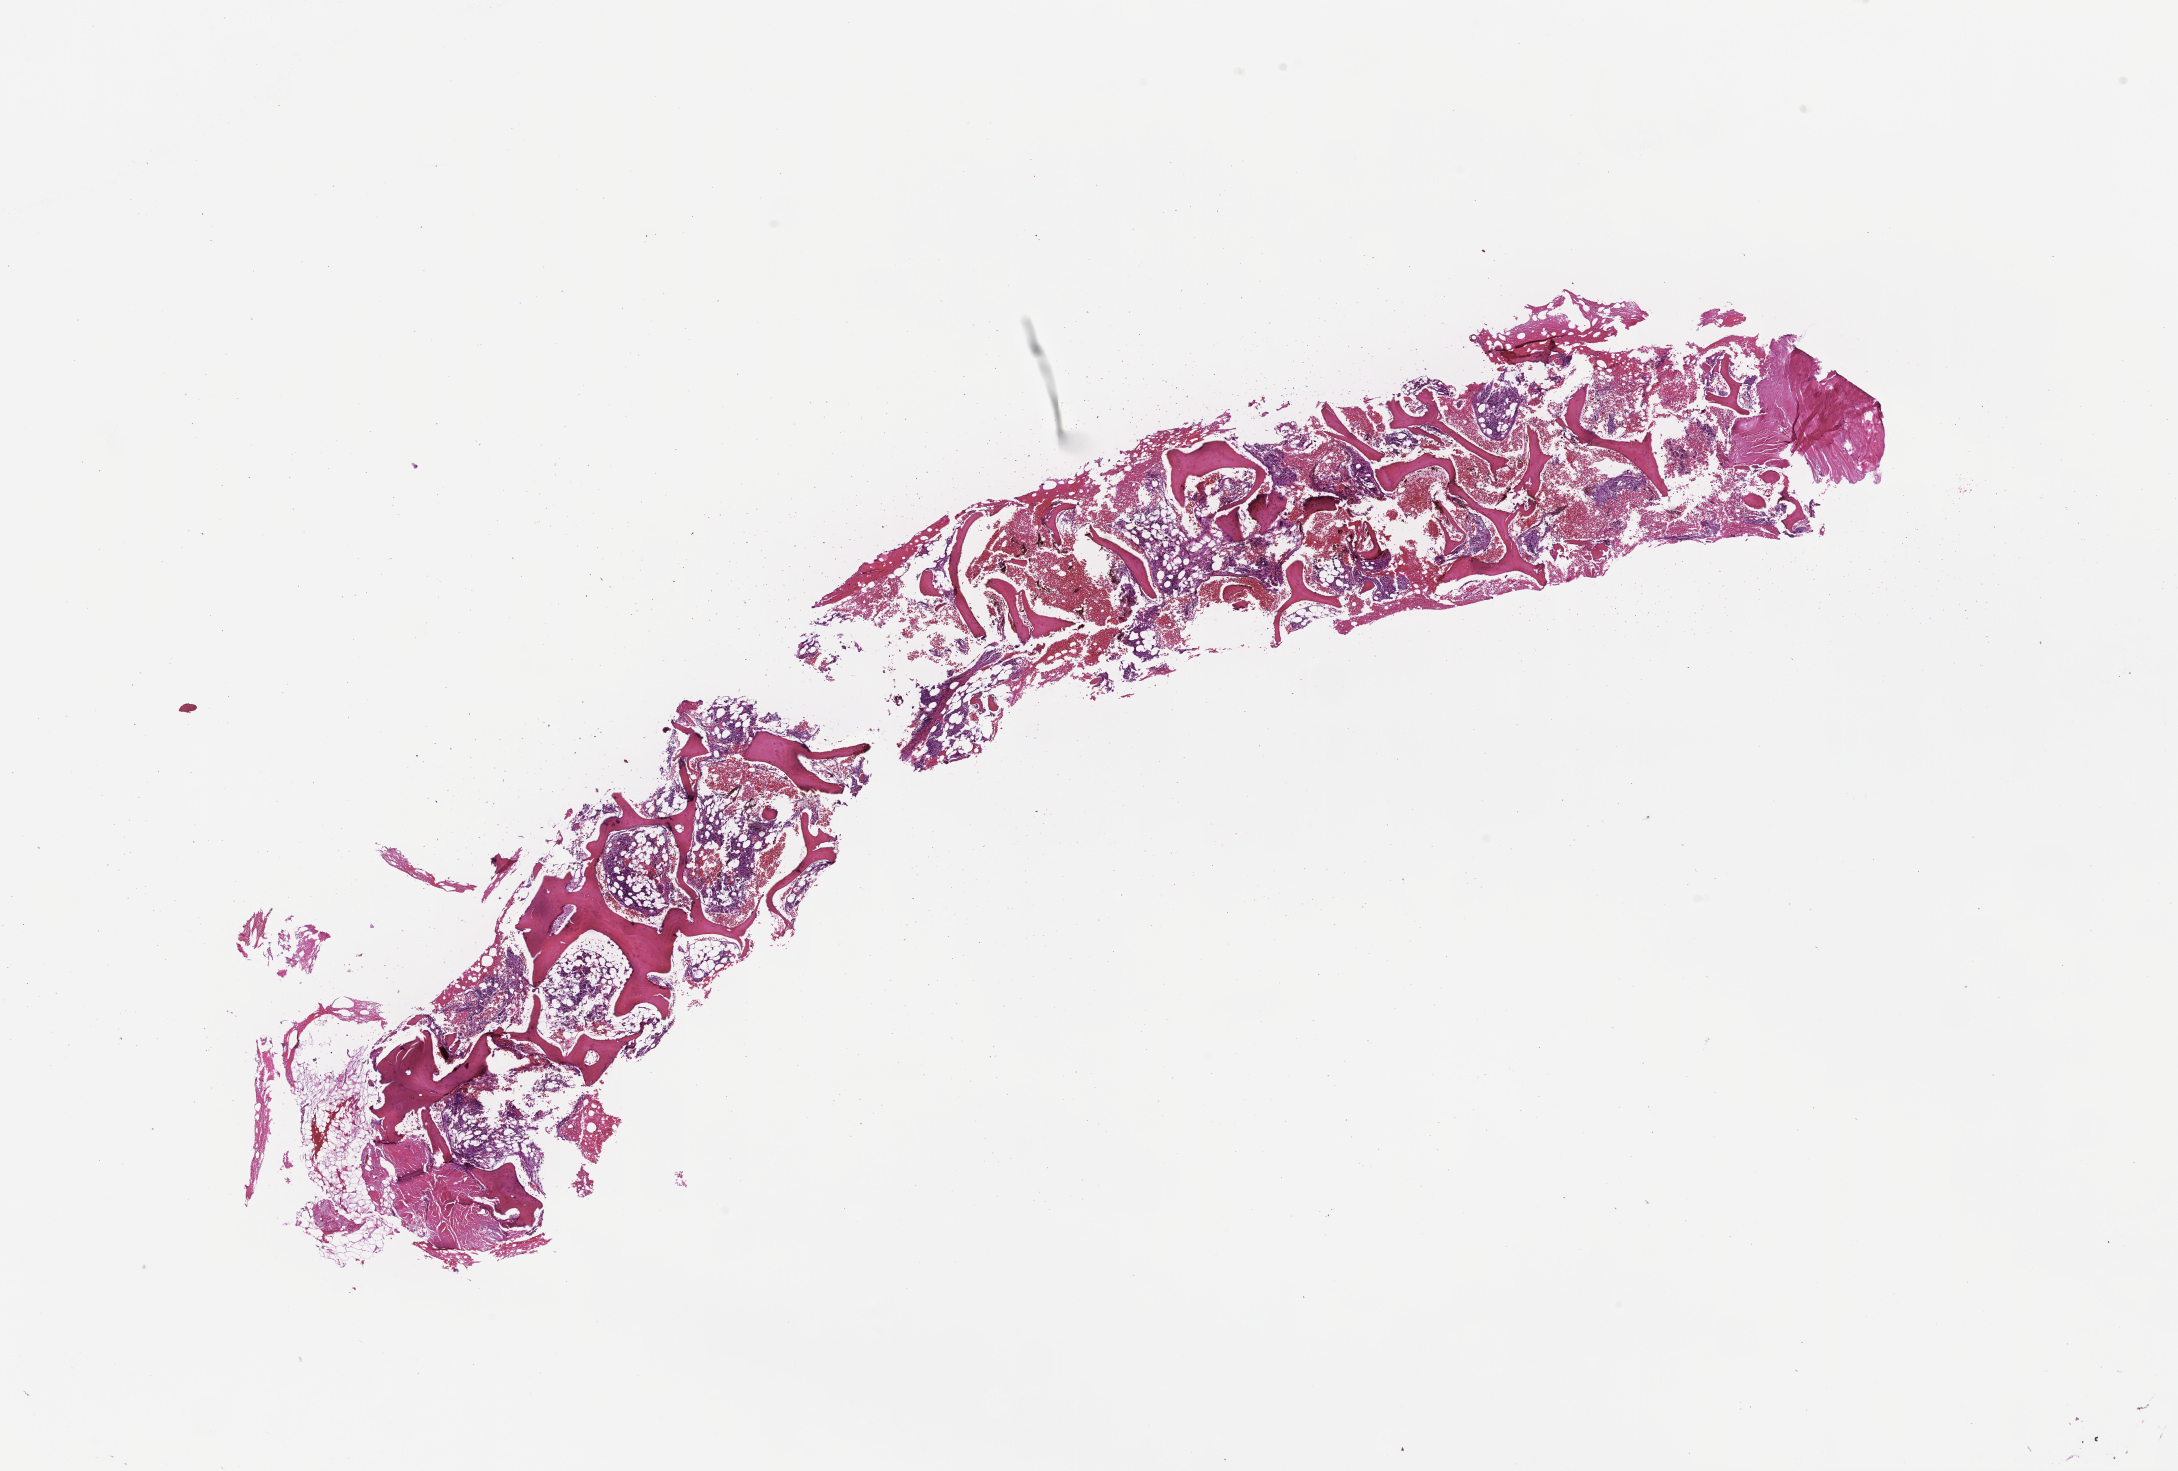
Digitized haematoxylin and eosin-stained section, whole scanned area (about 17.6 x 11.9 mm) shown as a low-resolution overview; FFPE section; site: bone marrow. Patient: female.
This section: primary tumor. Diagnosis: Plasma Cell Myeloma.